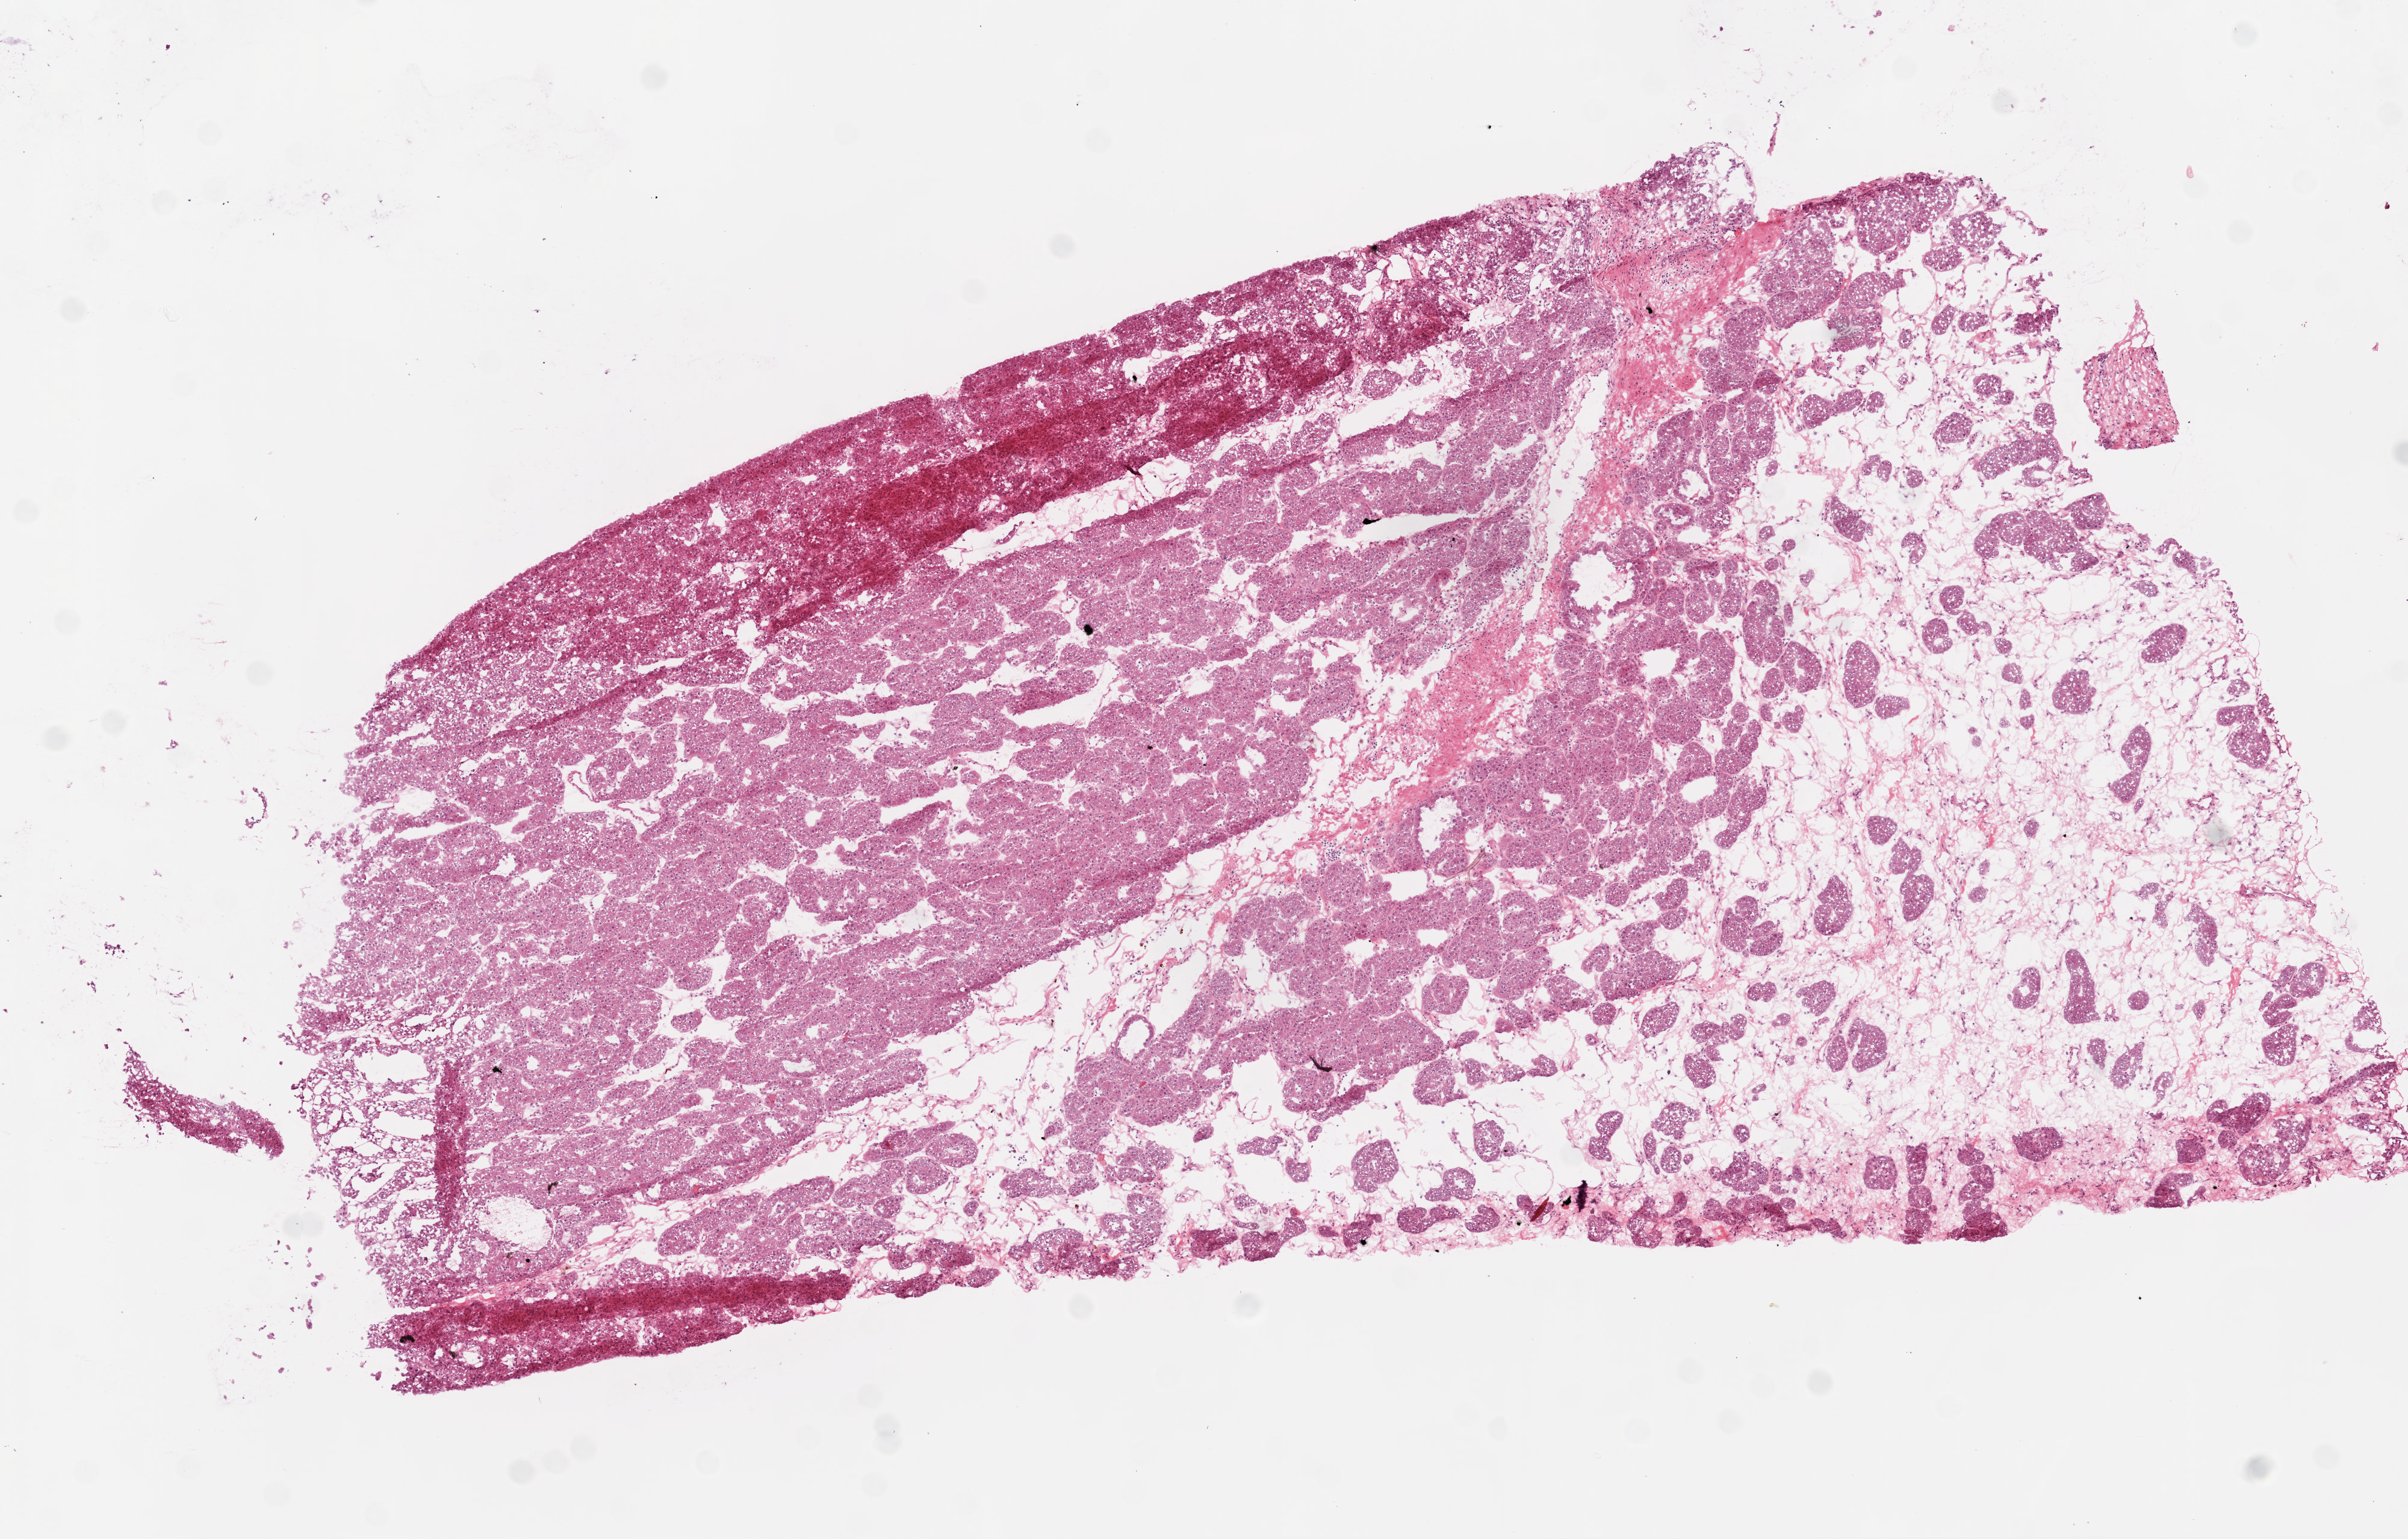
H&E-stained whole-slide image — shown as a low-resolution overview of the whole scanned area (about 8.0 x 5.1 mm, slide scanned at 20x); frozen section; primary tumour sample from the kidney. Patient: male, age at initial diagnosis 58 years. Histologic grade: G2 (moderately differentiated). Composition of this section per pathologist review: tumour cells 75%, tumour nuclei 80%, normal cells 0%, stromal cells 25%, necrosis 0%.
AJCC pathologic stage: I (7th edition). Pathologic diagnosis: Clear cell adenocarcinoma, NOS. Laterality: left.